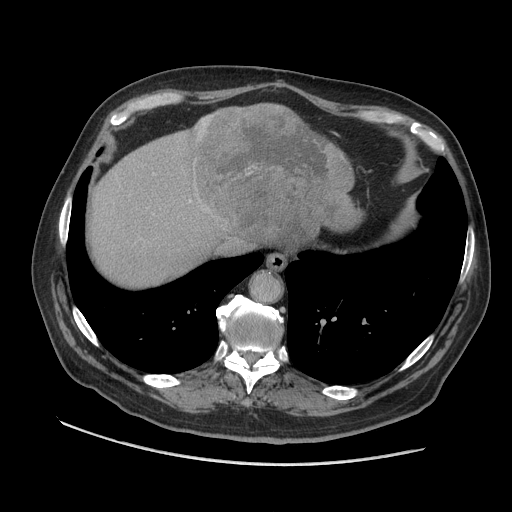
Contrast-enhanced abdominal CT (liver protocol), one axial slice. Soft-tissue window (W 400 / L 40 HU). 2.5 mm slice thickness. 512 × 512 image matrix. From the clinical record (not read from this slice): diagnosis: hepatocellular carcinoma (patient treated with transarterial chemoembolisation; whether this scan precedes or follows treatment is not stated here); TNM stage (as recorded): Stage-I; Child-Pugh class: A.
Structures marked on this image (semi-automatic segmentation, software-assisted and operator-edited):
- liver parenchyma outside the tumour (the mass and vessels are separate outlines, so this box may not span the whole liver): bounding box (x1, y1, x2, y2) in pixels: (90, 104, 300, 286)
- mass: (191, 104, 363, 244)